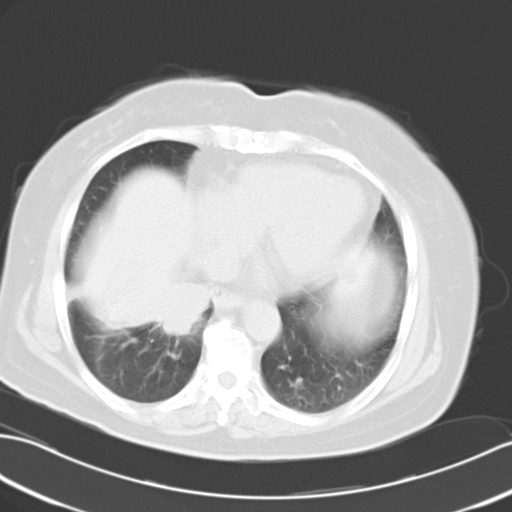
Chest CT, one axial slice. Position 9 of 24 along the scan axis. Lung window (W 1500 / L -600 HU). 10 mm slice thickness. 512 × 512 image matrix, field of view 353 × 353 mm. Patient: female, 63 years. Case-level facts recorded for this patient, not image findings: clinical TNM (as recorded): T3 N0 M0.
Annotated regions visible in this slice (rectangle marked by the reading radiologist):
- lung tumour (recorded histology: adenocarcinoma): bounding box [x1, y1, x2, y2] px = [80, 283, 212, 344]